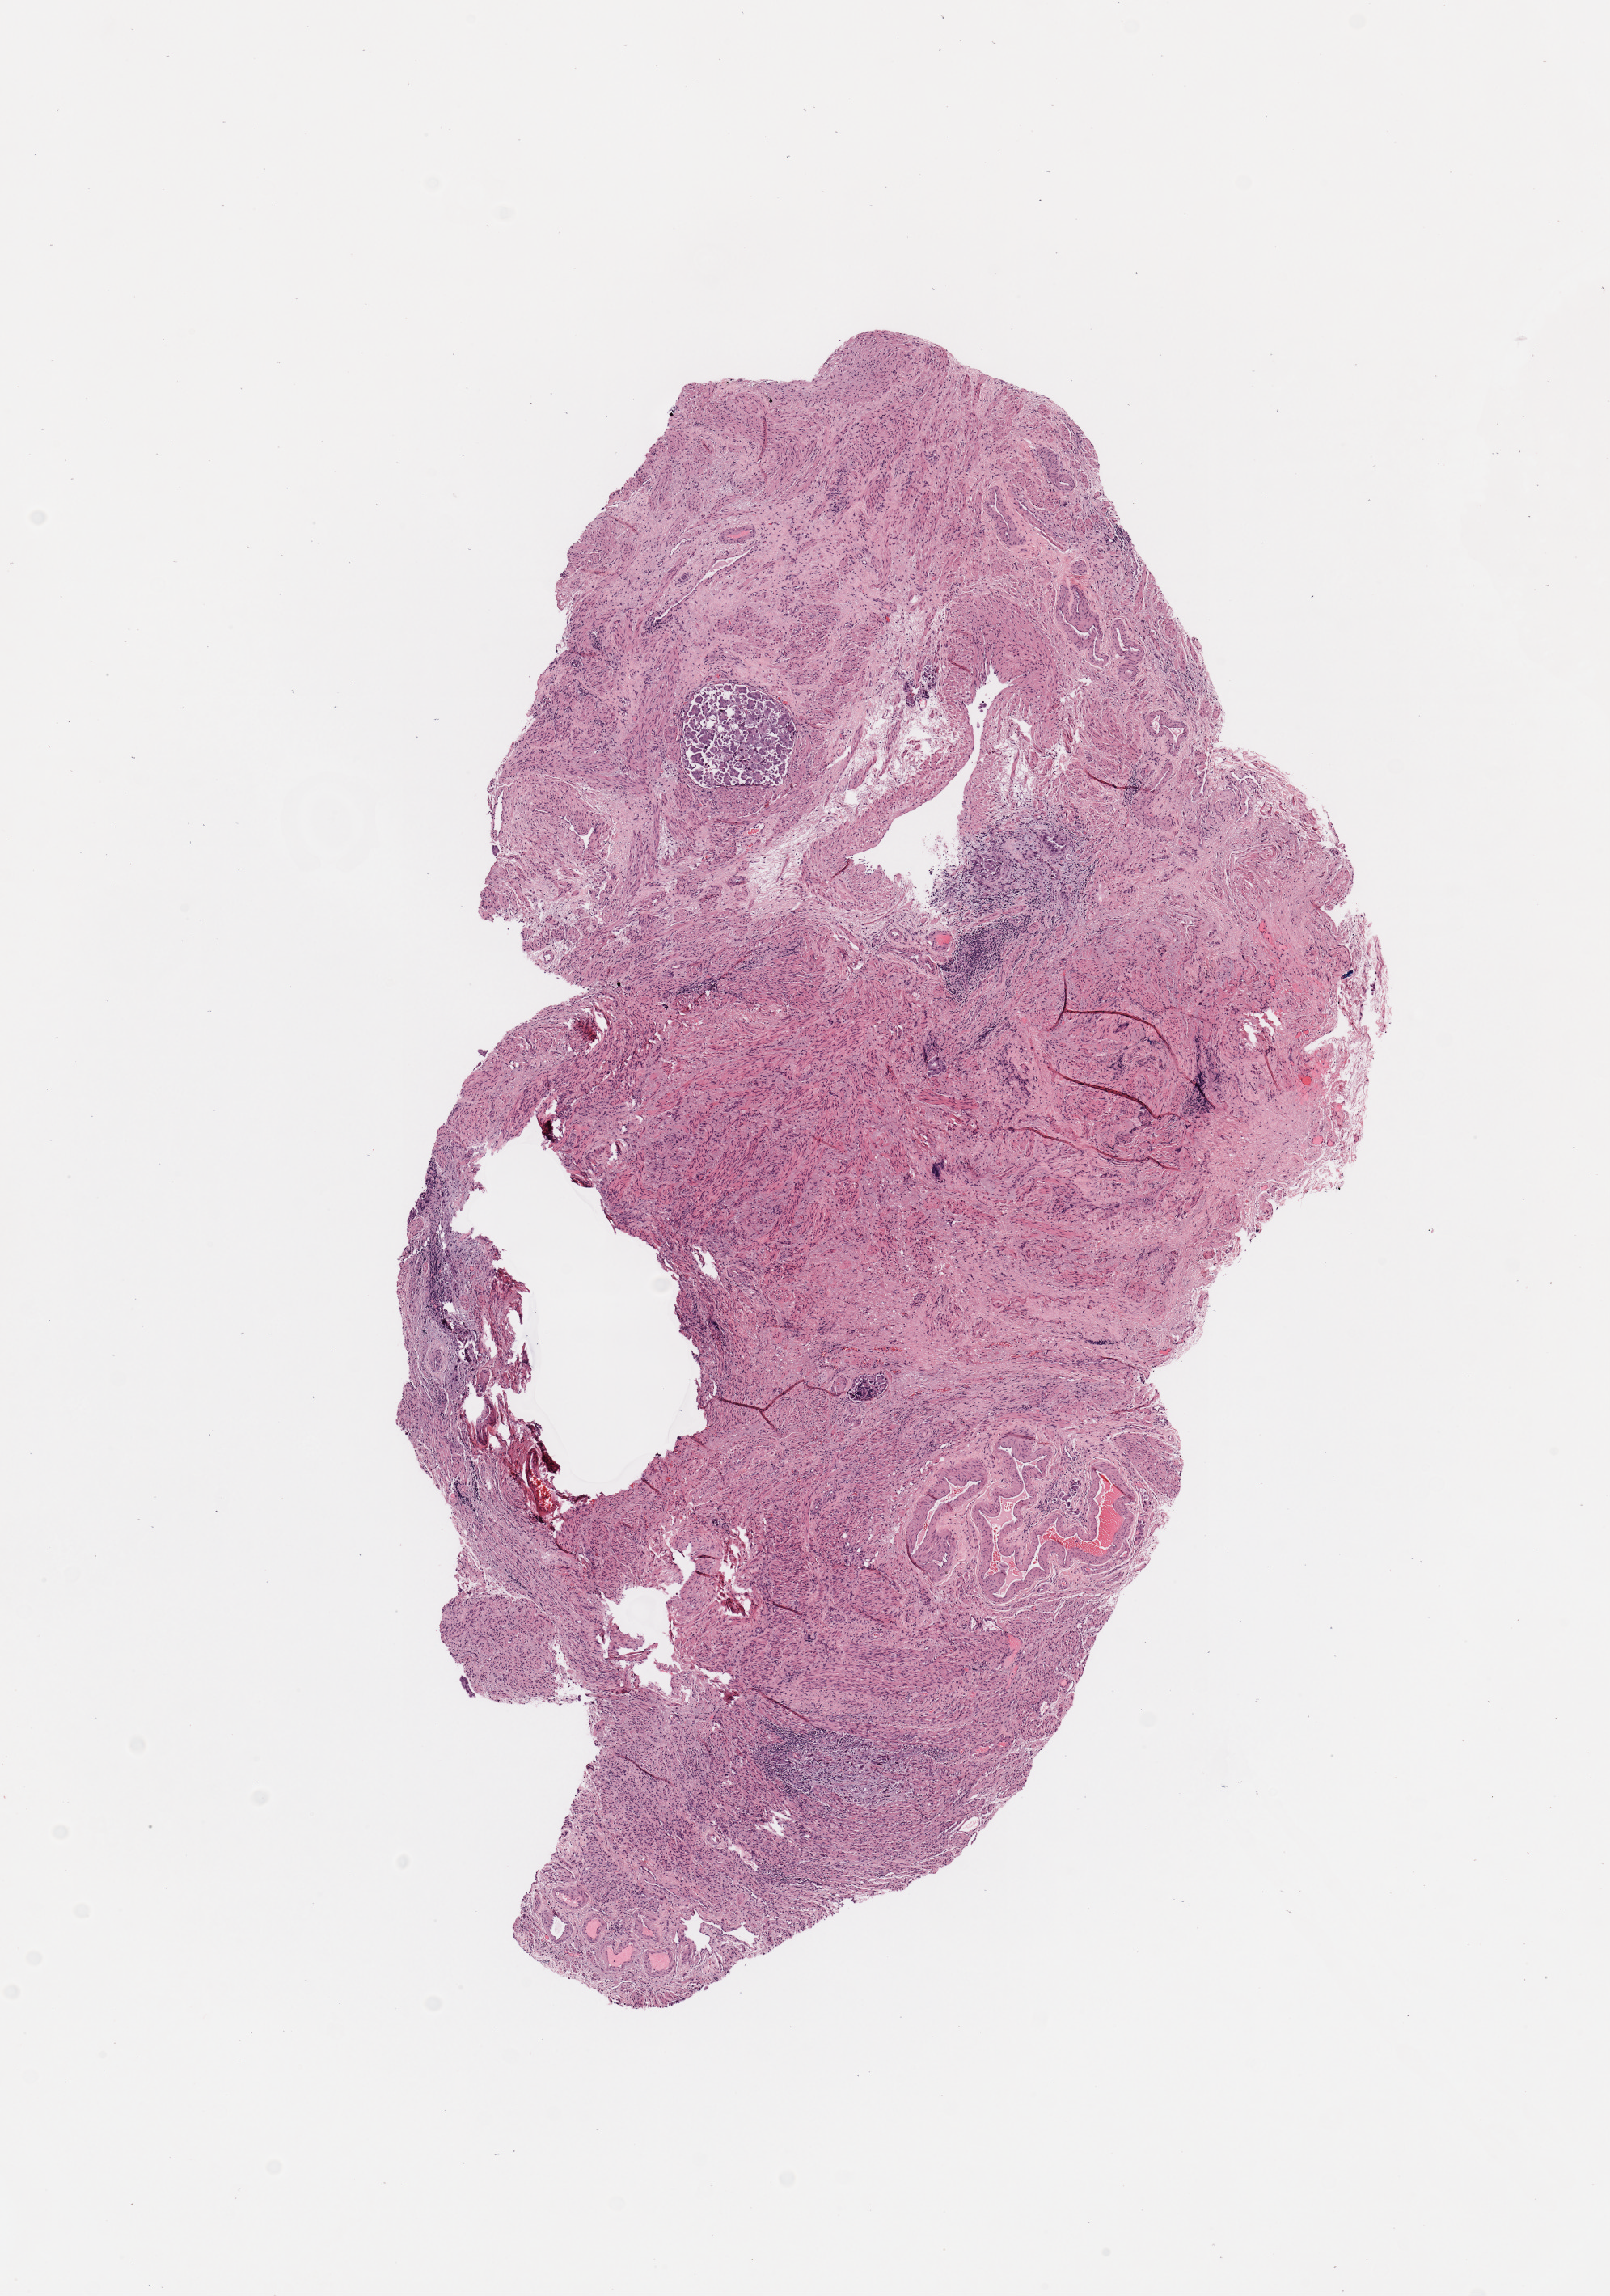
H&E whole-slide image — whole scanned area (about 7.9 x 11.2 mm) shown as a low-resolution overview; uterus, normal (non-tumour) tissue. 67-year-old female patient.
This section: normal (non-tumour) tissue from the same patient. Patient diagnosis: Endometrioid adenocarcinoma, NOS.